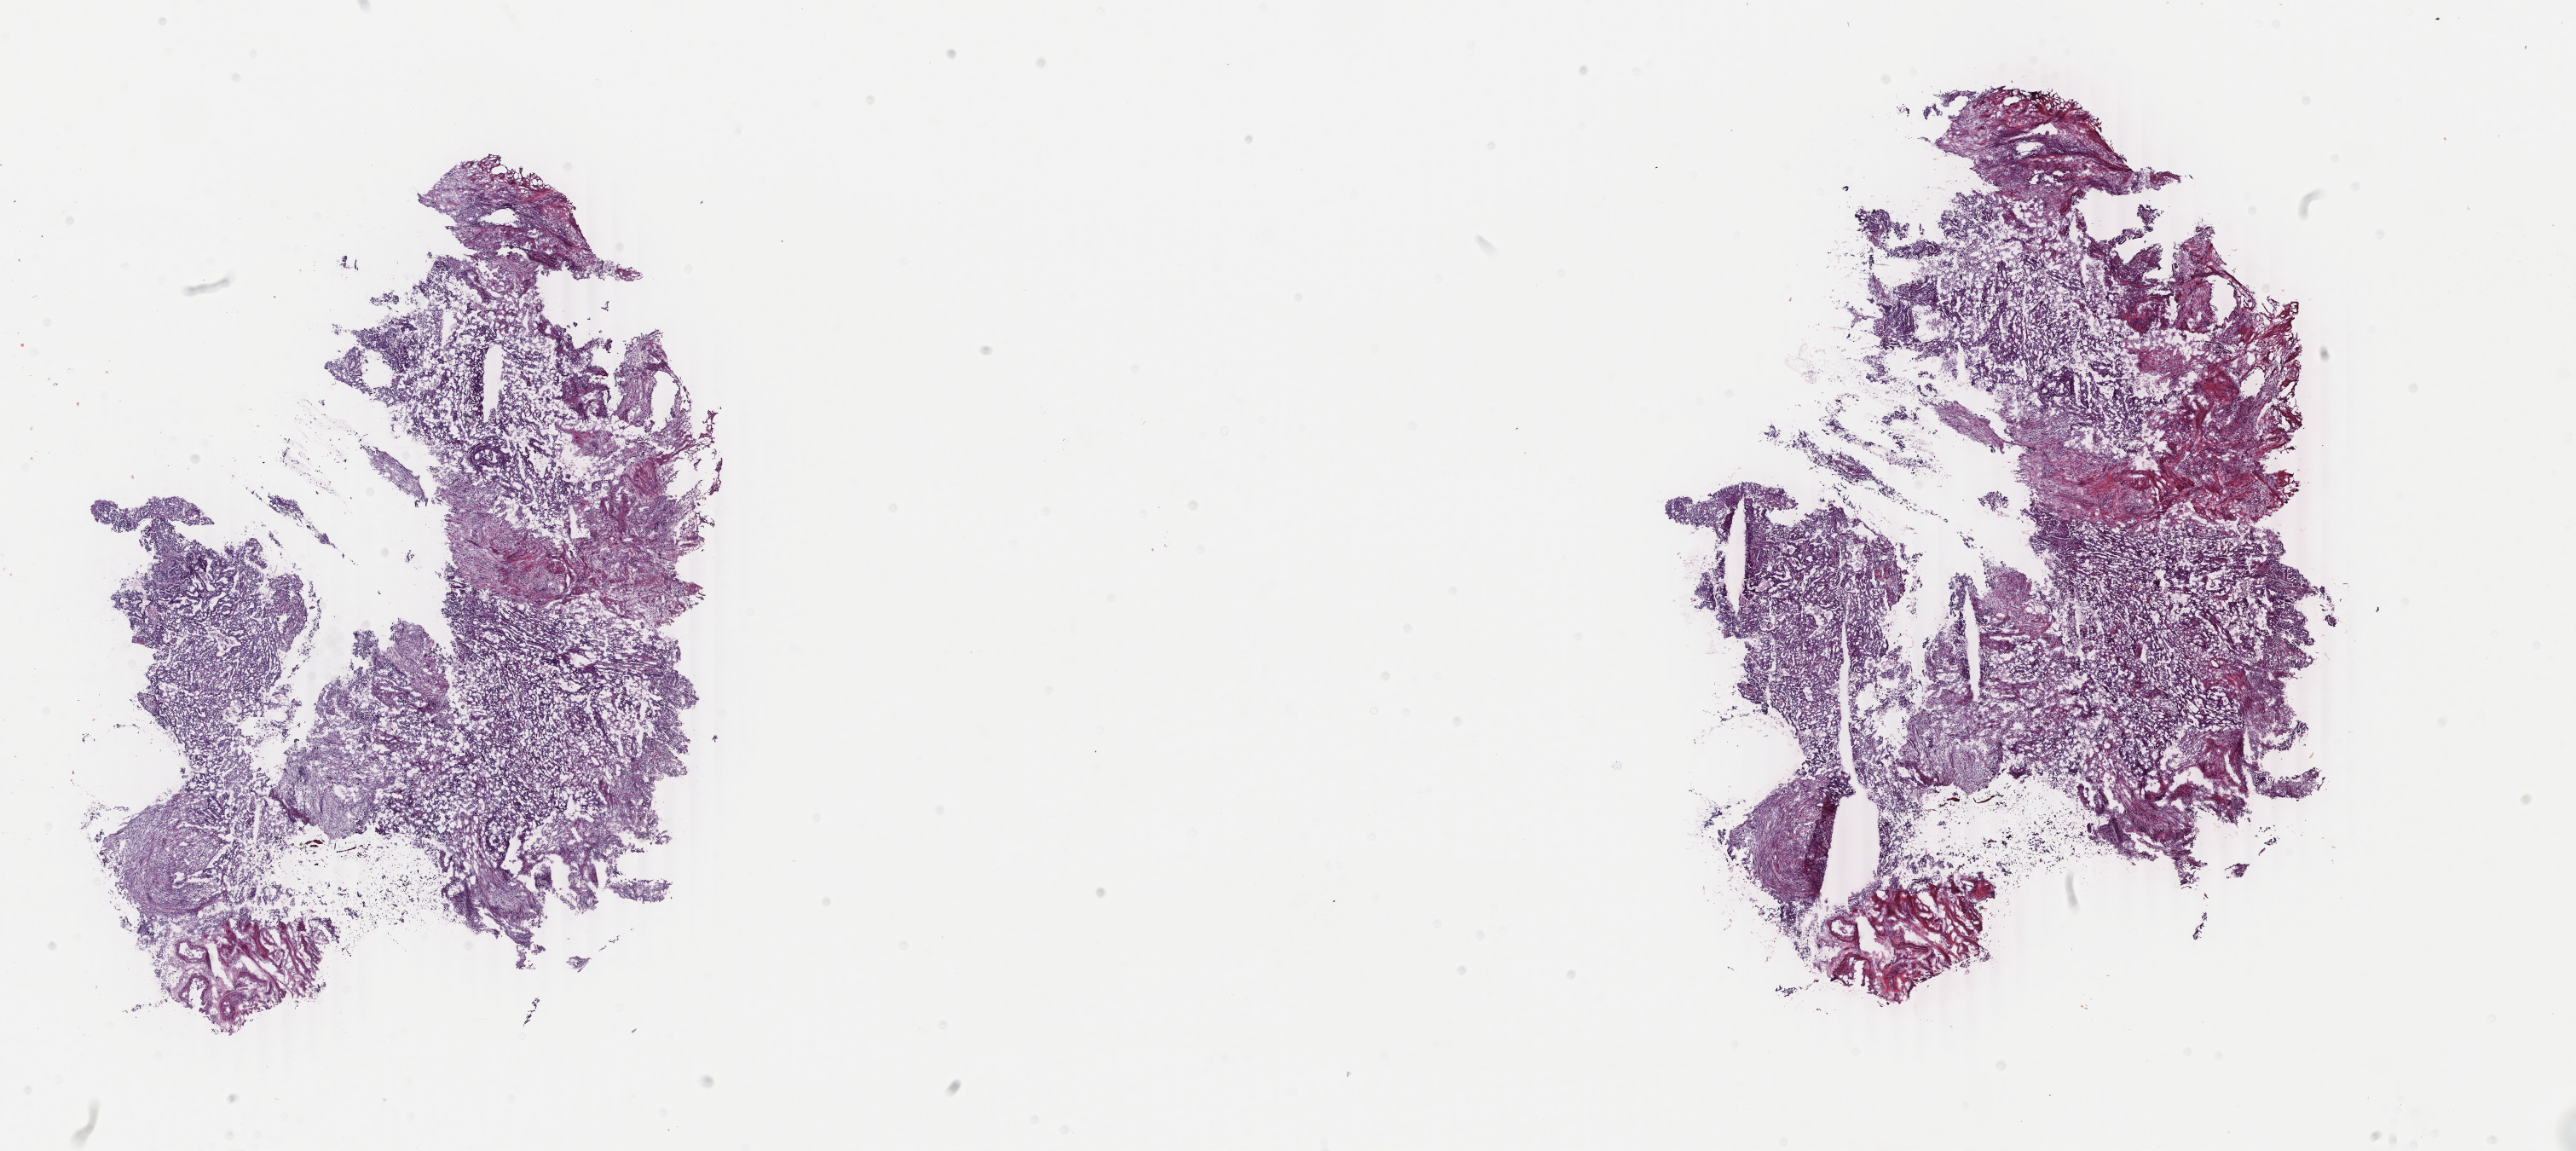
Hematoxylin and eosin (H&E) stained whole-slide image, shown as a low-resolution overview of the whole scanned area (about 24.0 x 10.7 mm, from a 40x scan), frozen section from the top of the tissue portion, uterus, primary tumour sample. Patient: female, age at initial diagnosis 60 years. Histologic grade: G2 (moderately differentiated). Composition of this section per pathologist review: tumour cells 80%, tumour nuclei 70%, normal cells 0%, stromal cells 20%, necrosis 0%. Inflammatory infiltration, as recorded: lymphocyte infiltration 0%, monocyte infiltration 0%, neutrophil infiltration 0%.
- FIGO stage: IIIA
- lymph nodes positive (case pathology): 0 of 7 examined
- pathologic diagnosis: Endometrioid adenocarcinoma, NOS